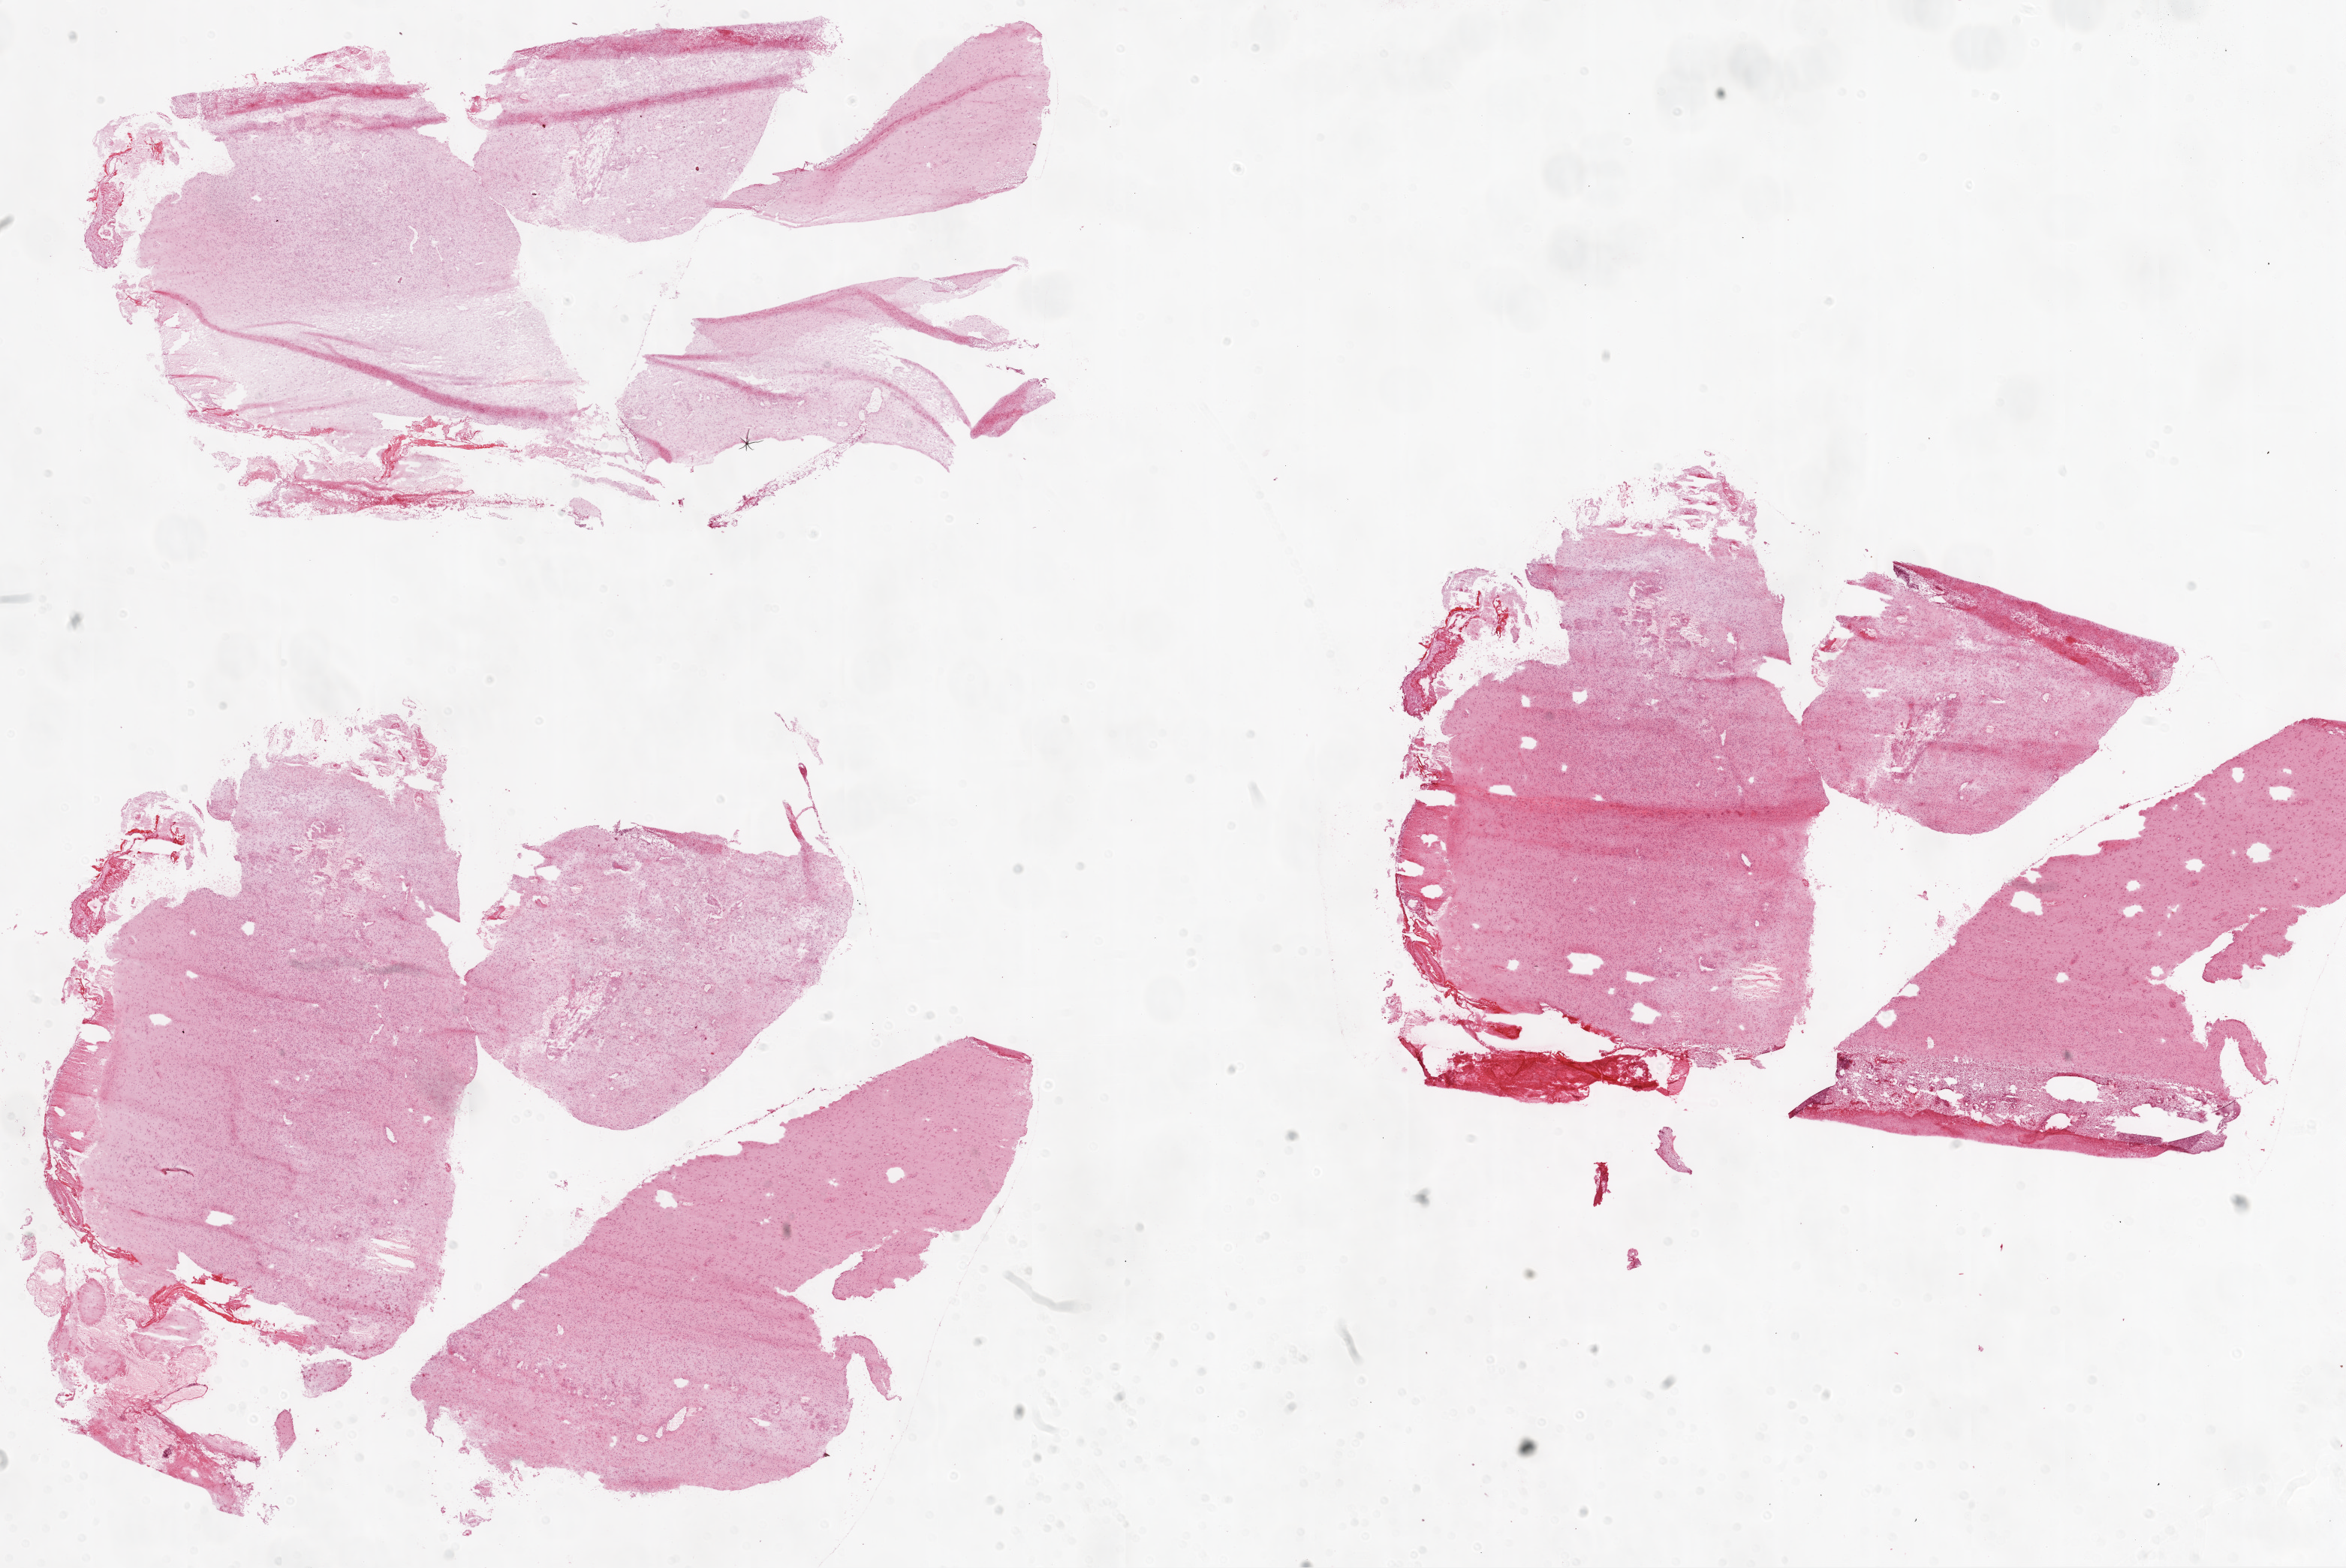
Whole-slide histology image, H&E-stained, whole scanned area (about 25.1 x 16.8 mm, slide scanned at 20x) shown as a low-resolution overview, frozen section from the top of the tissue portion, sample: primary tumour, brain. Patient: female, age at initial diagnosis 33 years.
Diagnosis: Glioblastoma.